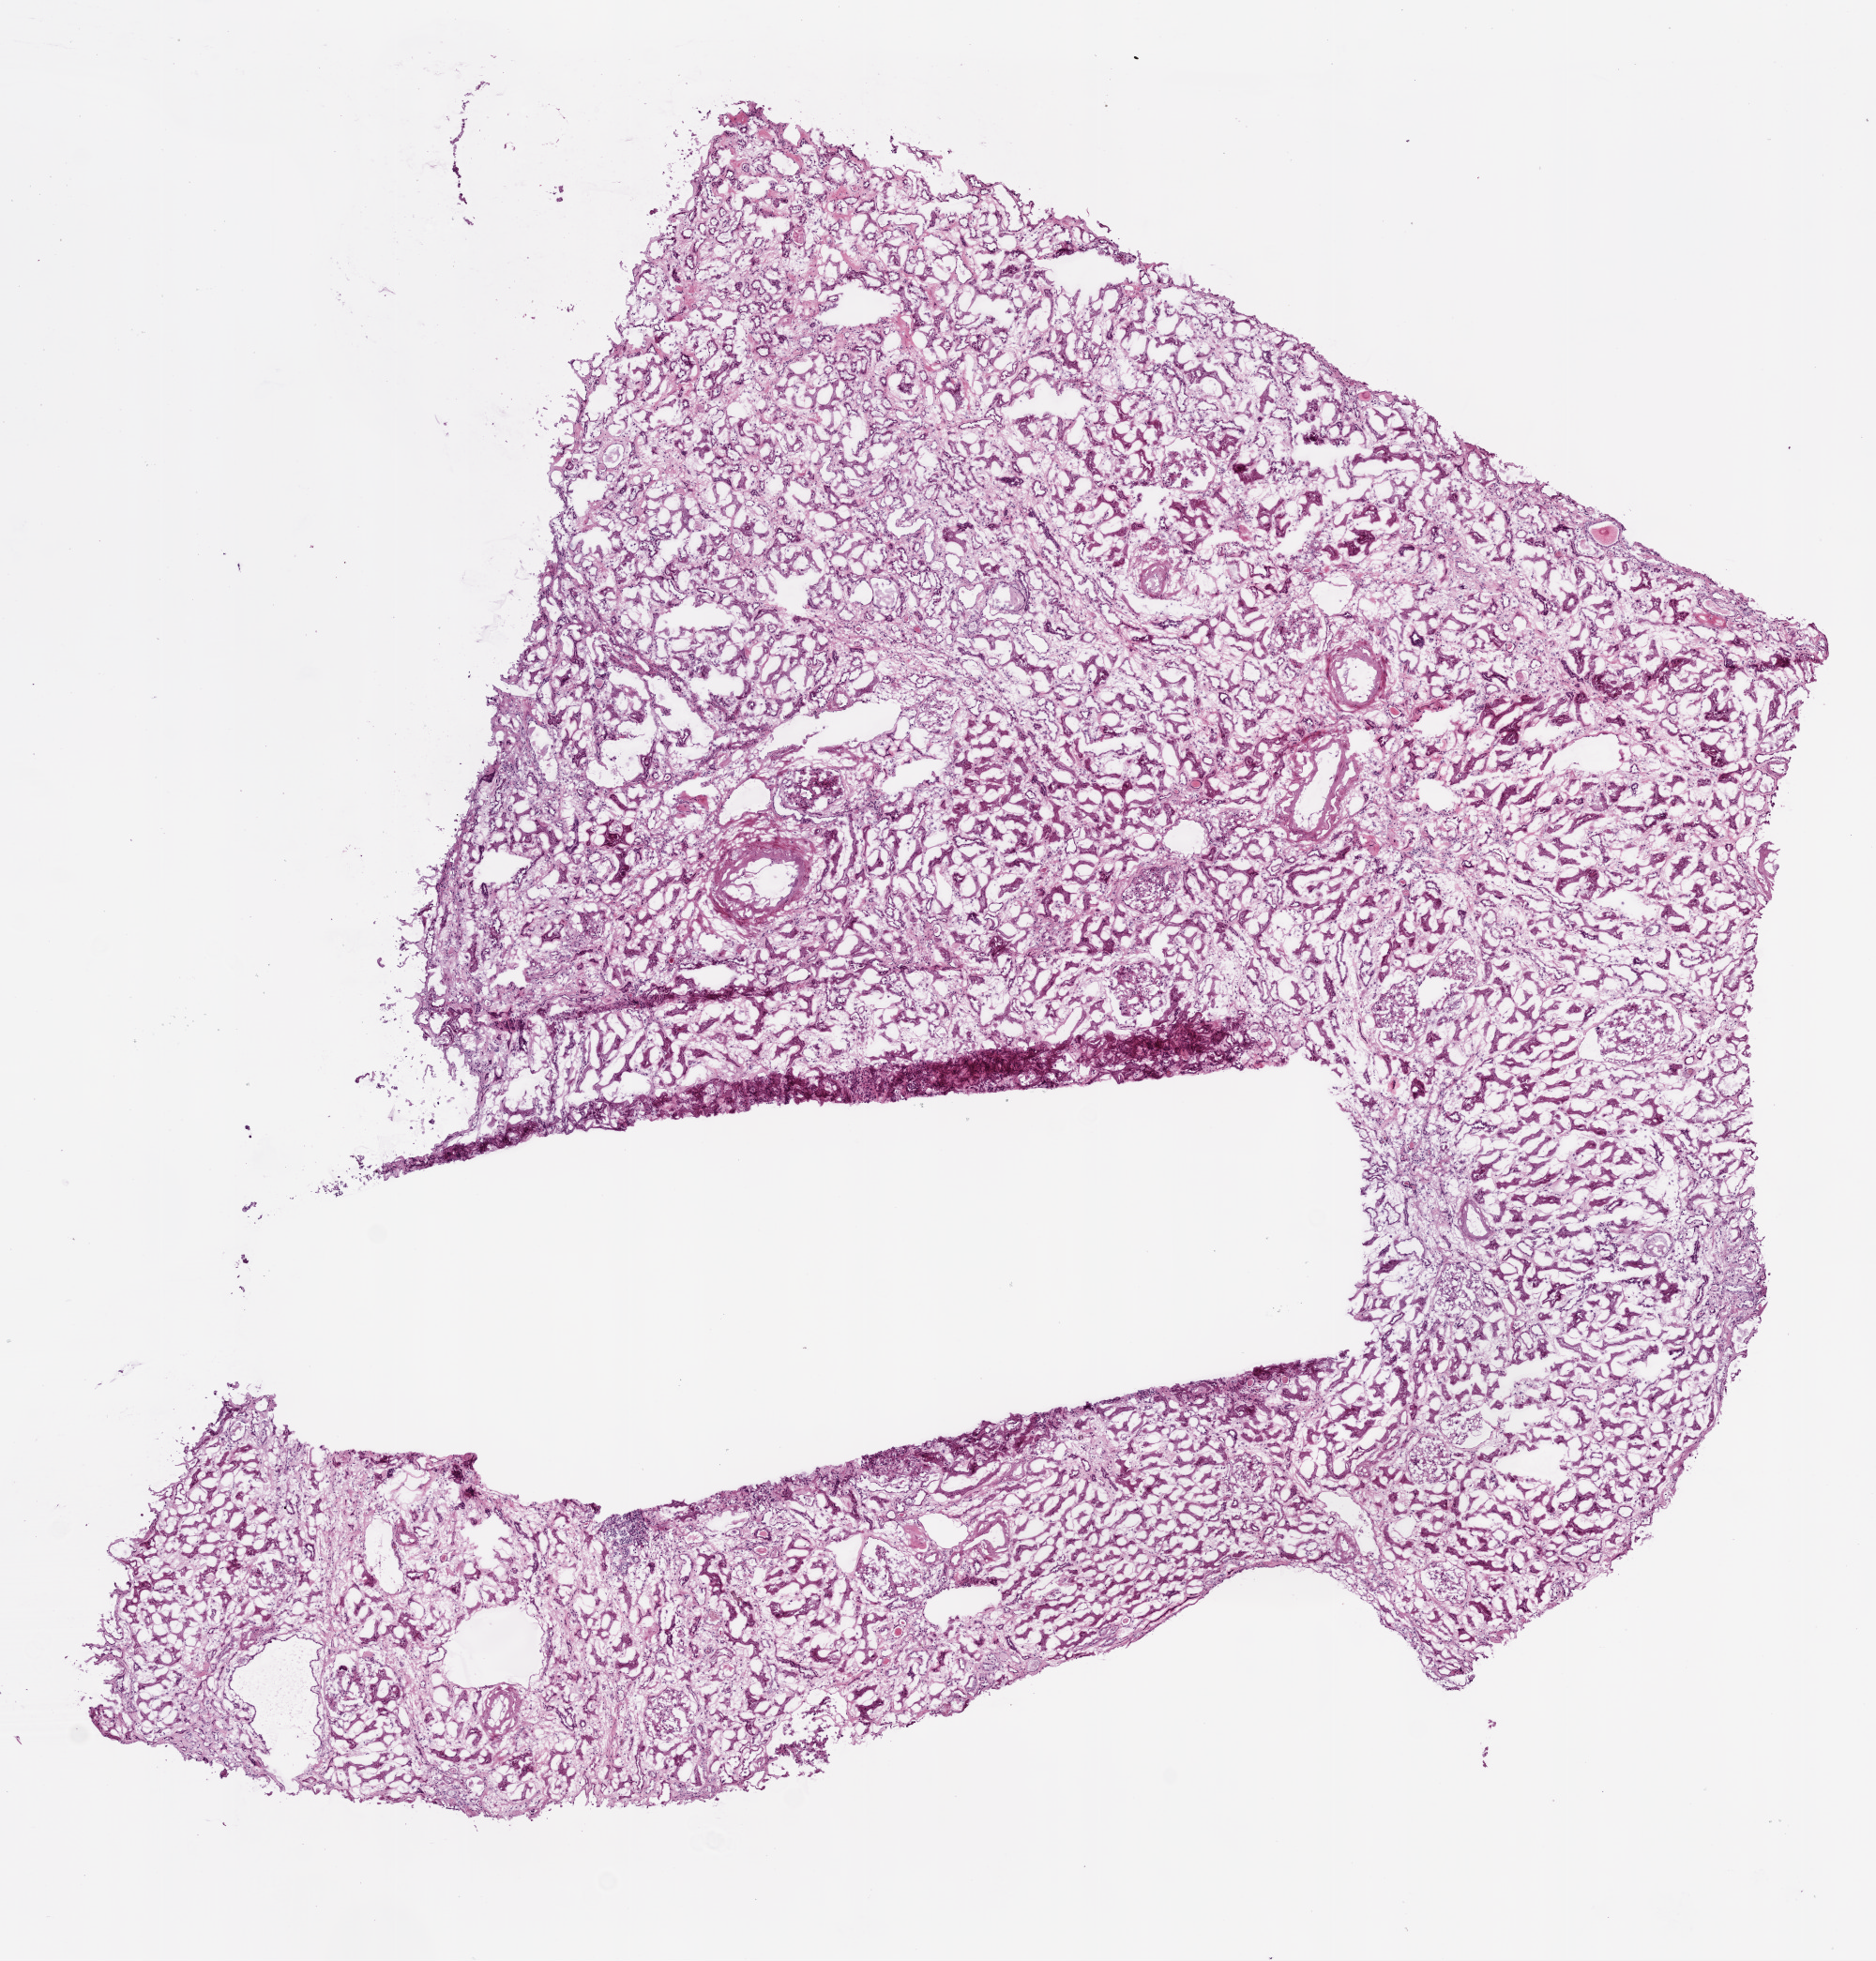
Digitized H&E-stained tissue section (whole slide), shown as a low-resolution overview of the whole scanned area (about 8.0 x 8.4 mm, acquisition: 20x scan), frozen section from the bottom of the tissue portion, solid tissue normal (non-tumour tissue) sample from the kidney. Patient sex: male.
• this section: solid tissue normal sample (biorepository sample class)
• patient diagnosis: Clear cell adenocarcinoma, NOS